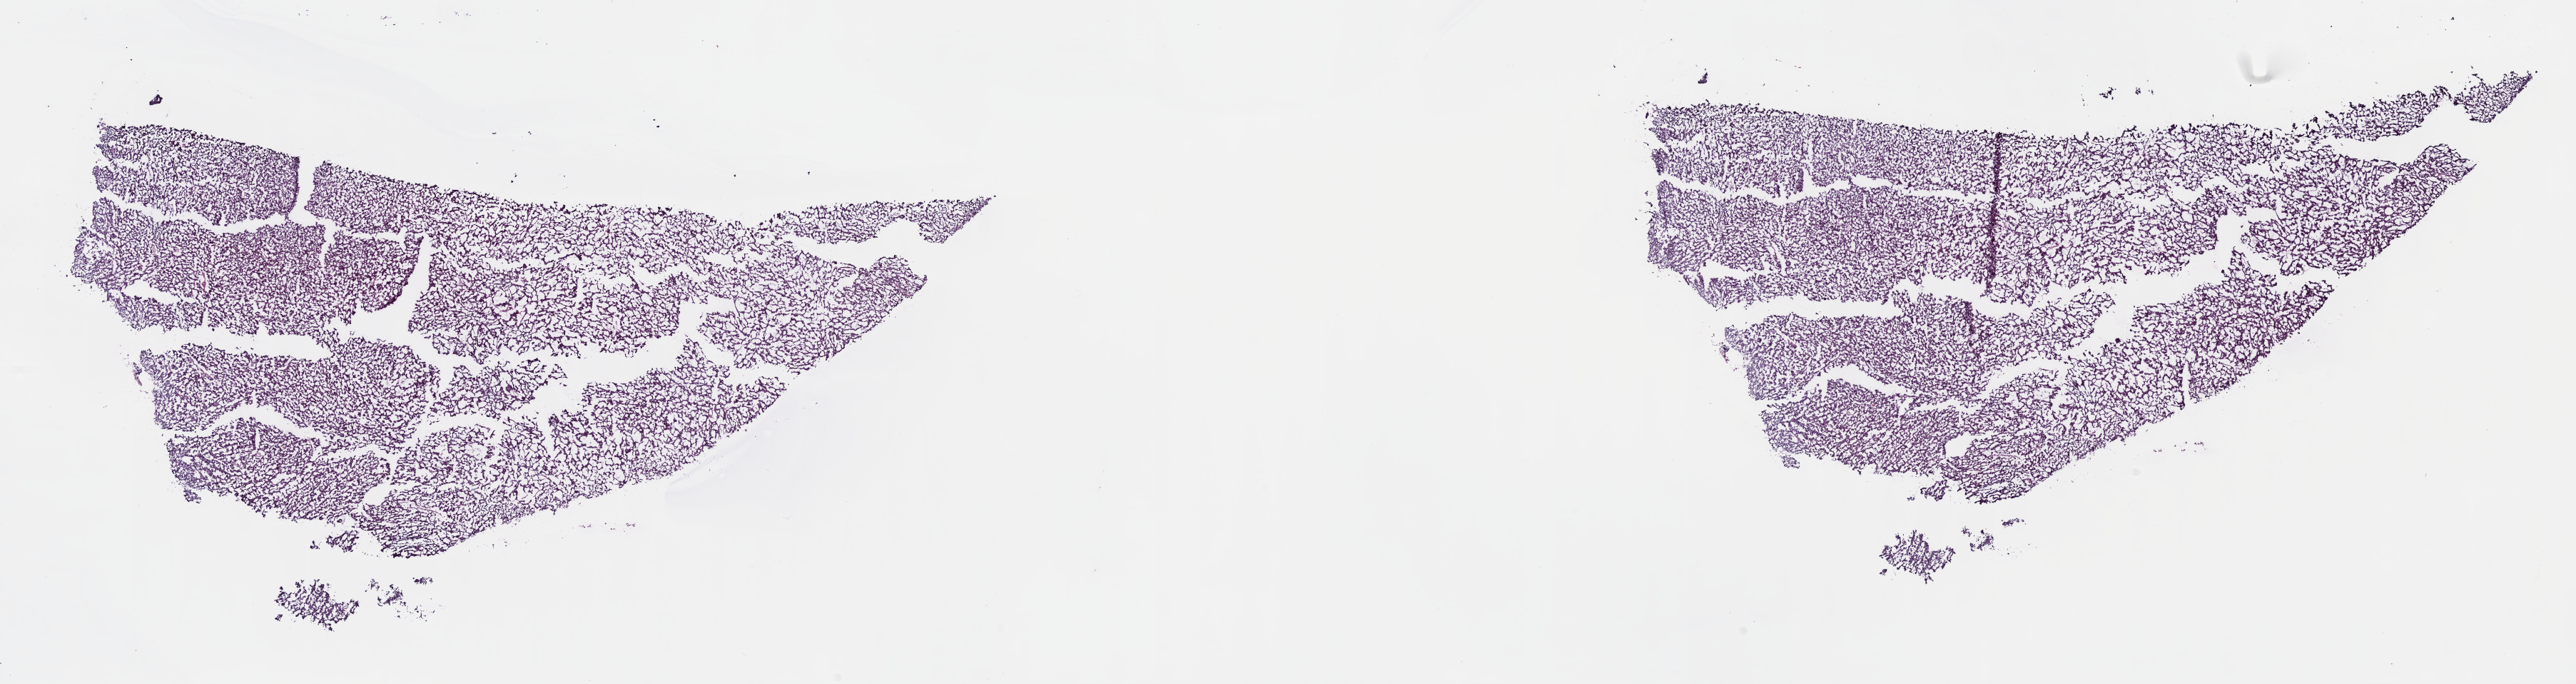
Hematoxylin and eosin (H&E) stained whole-slide image, whole scanned area (about 29.2 x 7.7 mm) shown as a low-resolution overview; frozen section from the top of the tissue portion; kidney, primary tumour sample. Male patient; age at initial diagnosis 59 years. Pathologist review of this section (percent, as recorded): tumour cells 100%, tumour nuclei 80%, normal cells 0%, stromal cells 0%, necrosis 0%. Inflammatory infiltration, as recorded: lymphocyte infiltration 1%, monocyte infiltration 2%, neutrophil infiltration 0%.
* pathologic diagnosis: Papillary adenocarcinoma, NOS
* AJCC pathologic stage: II (6th edition)